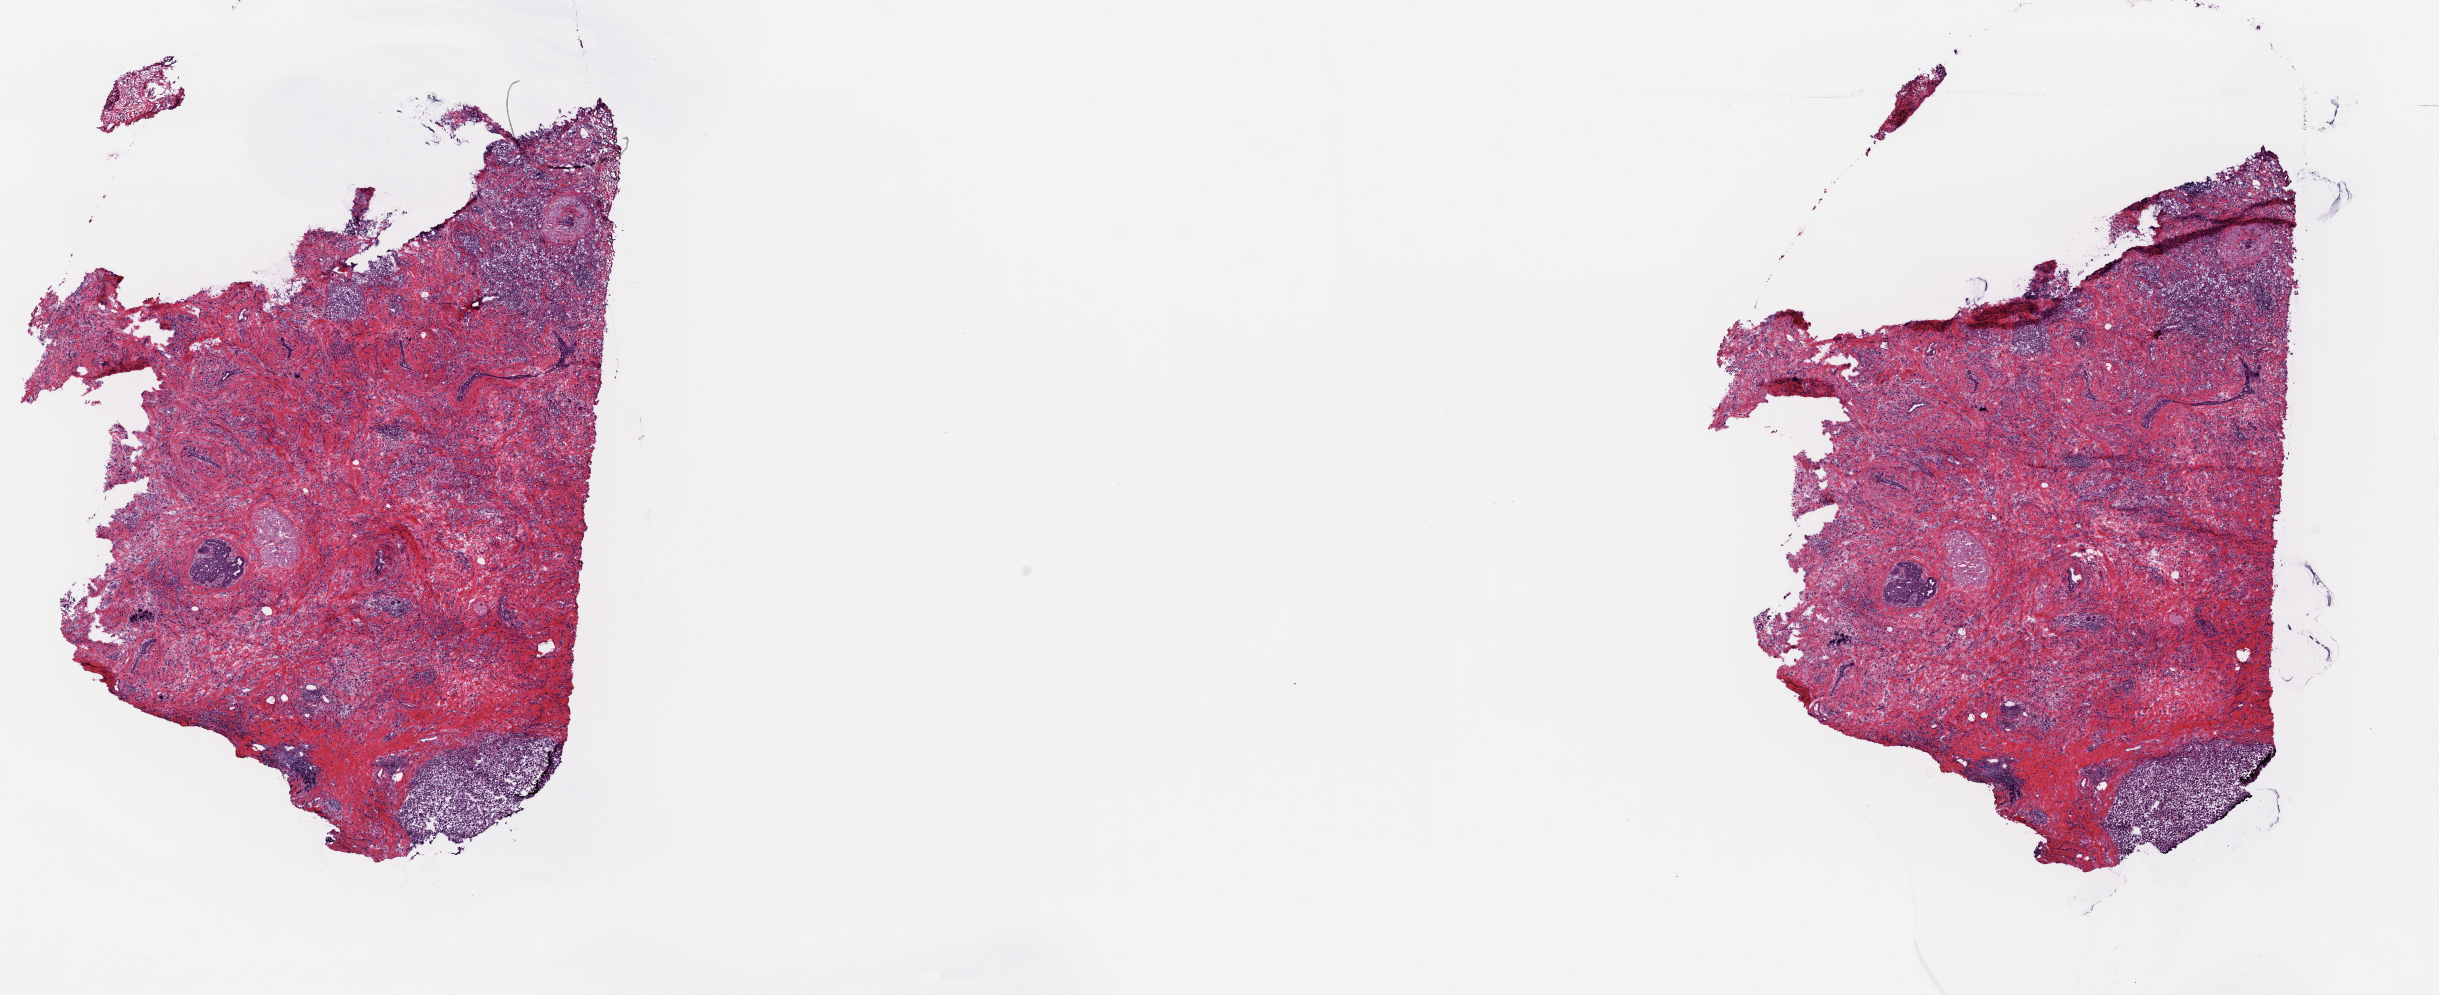
Whole-slide histology image, Hematoxylin and eosin (H&E) stained, a low-resolution overview of the entire scanned area, about 19.3 x 7.9 mm. Frozen section from the top of the tissue portion. Sample: primary tumour, breast. Patient: female, age at initial diagnosis 65 years. Pathologist review of this section (percent, as recorded): tumour cells 85%, tumour nuclei 70%, normal cells 0%, stromal cells 15%, necrosis 0%. Inflammatory infiltration, as recorded: lymphocyte infiltration 0%, monocyte infiltration 0%, neutrophil infiltration 0%.
* AJCC pathologic stage: IIA (6th edition)
* pathologic diagnosis: Lobular carcinoma, NOS
* lymph nodes positive (case pathology): 0 of 1 examined
* TNM: T2 N0 MX